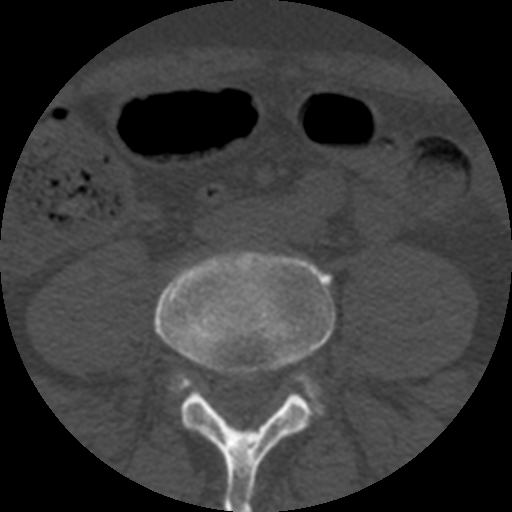
CT including the spine, one axial slice; position 83 of 508 along the scan axis; 120 kVp; bone window (W 1800 / L 400 HU); 512 × 512 image matrix, field of view 160 × 160 mm. Patient age 57 years. From the clinical record (not read from this slice): primary cancer: prostate.
Outlined on this slice (semi-automatically segmented with operator editing):
- L4 vertebra: bounding box <154,249,336,512> (left, top, right, bottom; pixels)
- L5 vertebra: <171,375,320,396>